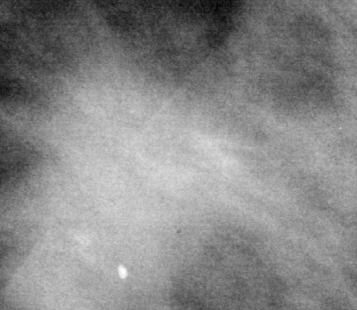
Cropped region of a digitized screen-film mammogram centred on a radiologist-marked abnormality, left breast, MLO view.
Finding: mass, shape round, margins spiculated; BI-RADS assessment category 5; pathology (as recorded): malignant.